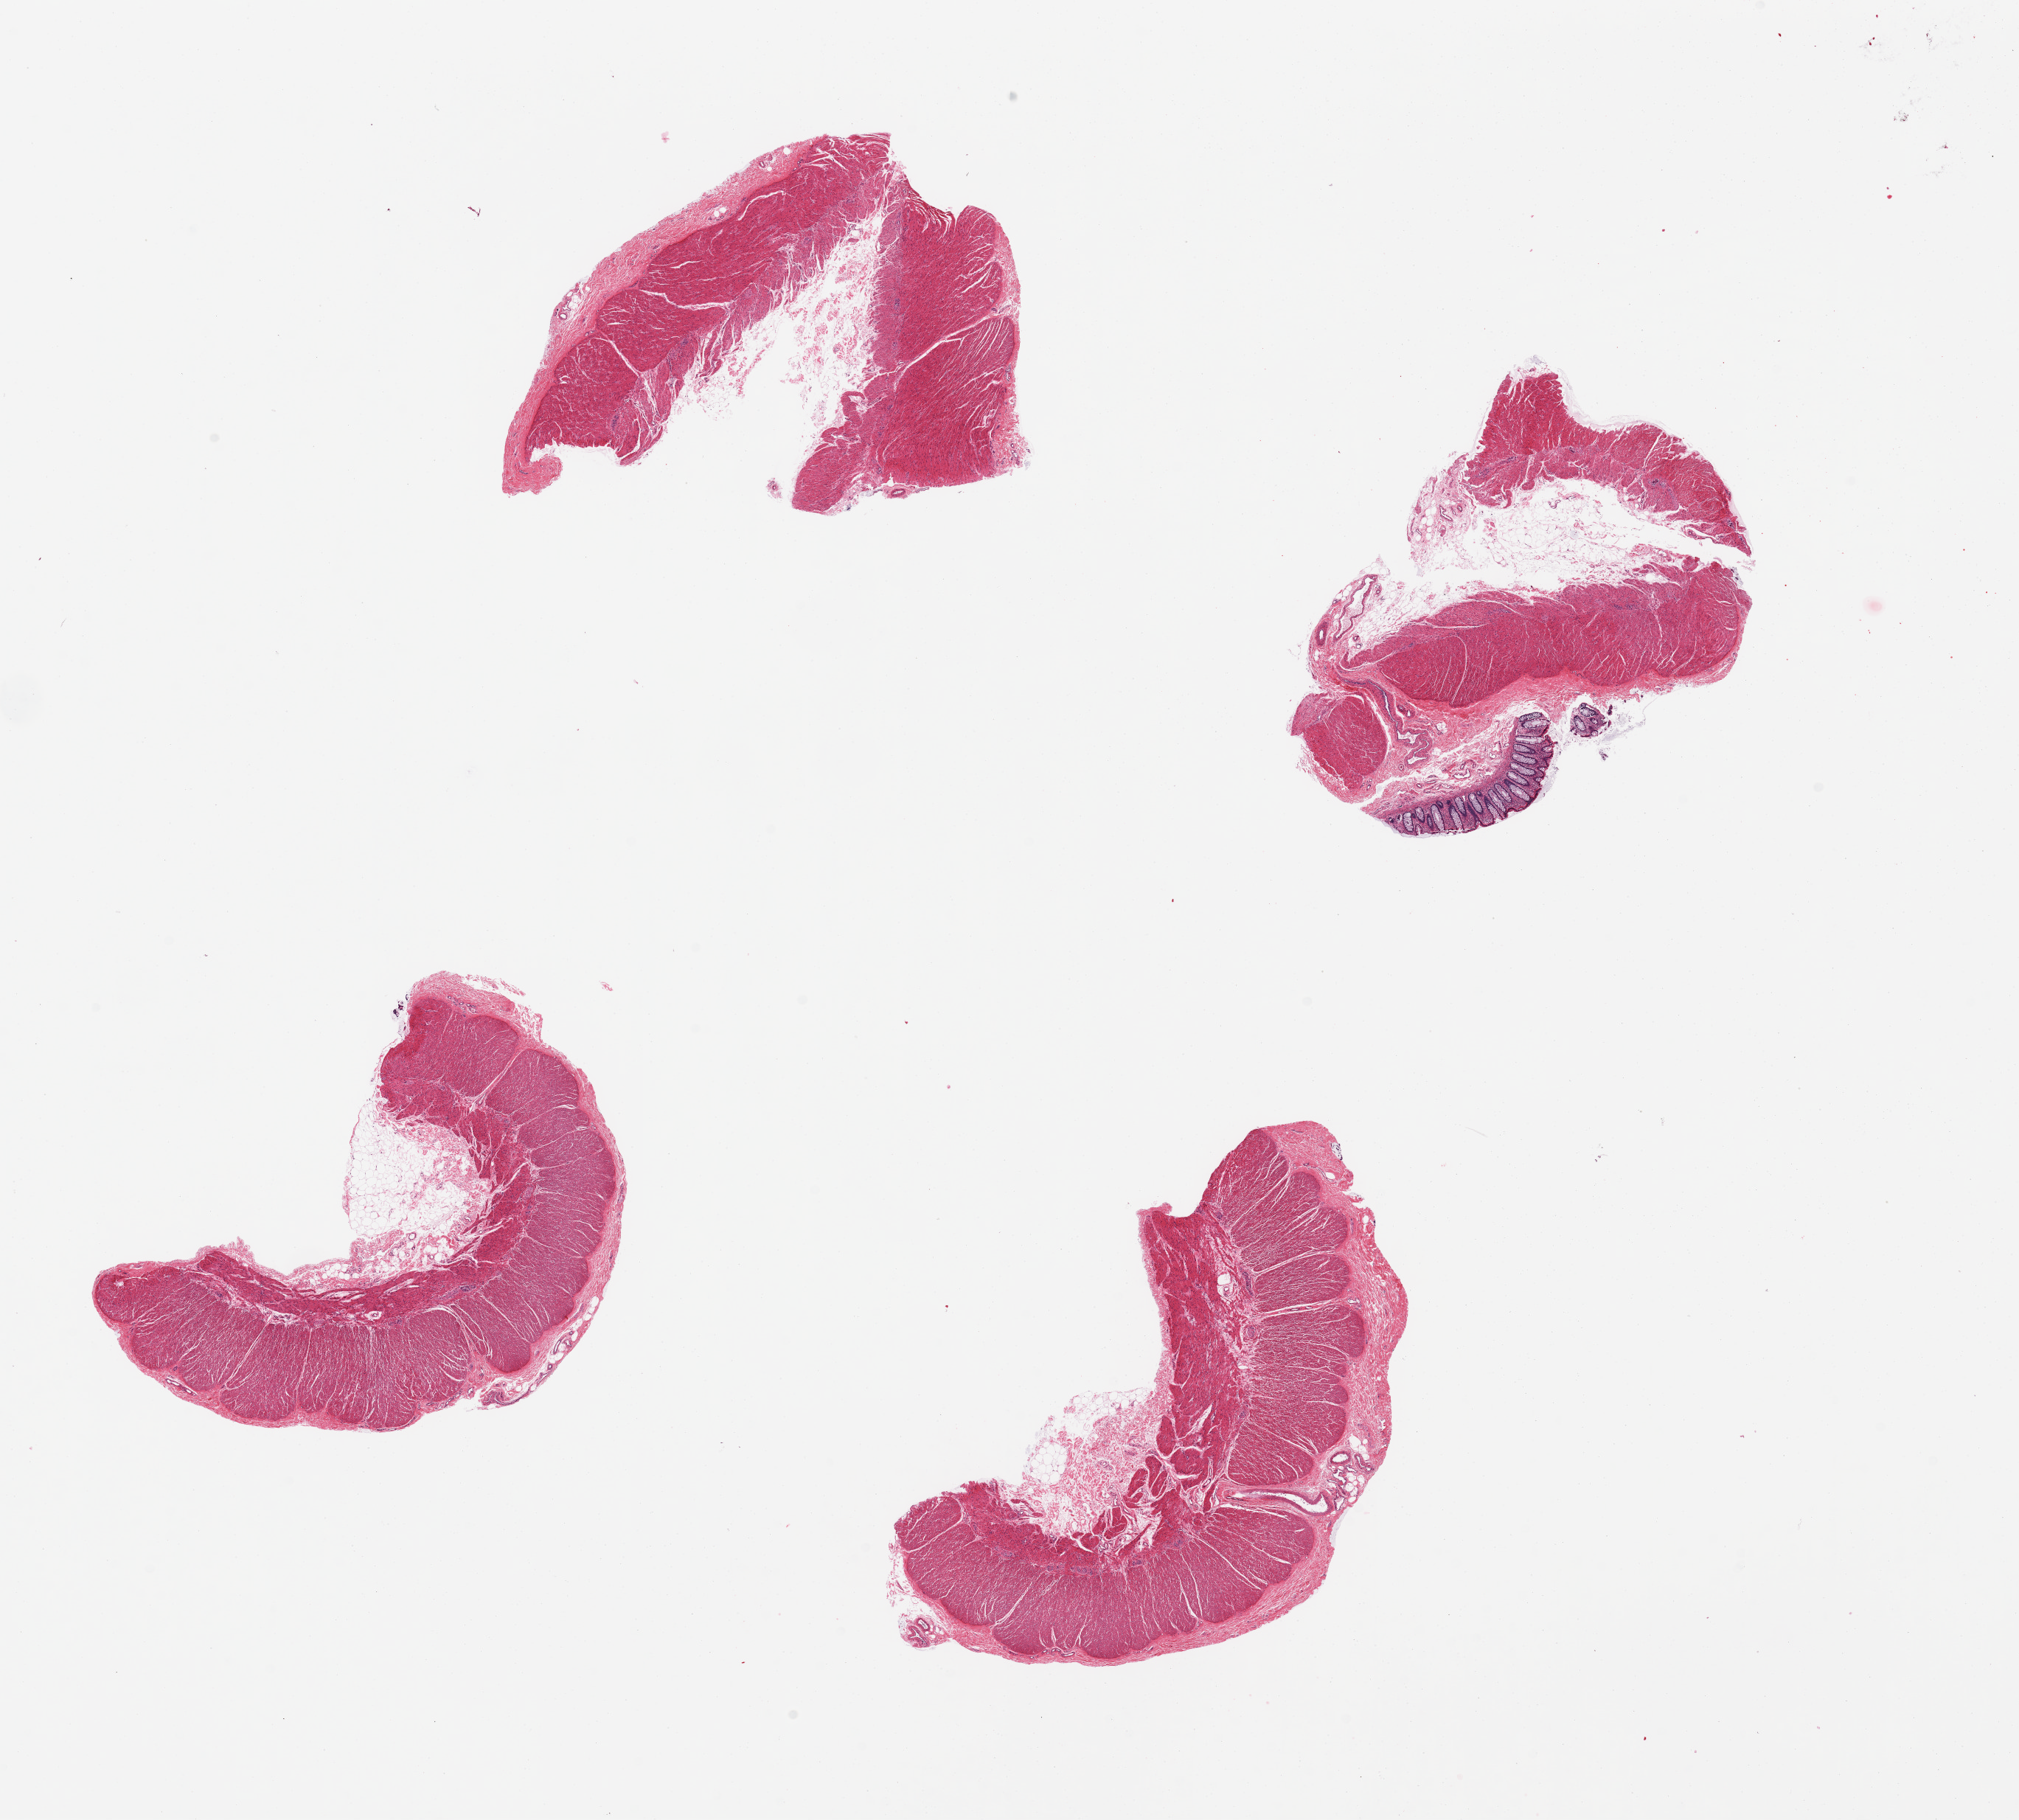
Whole-slide image, H&E stain — a low-resolution overview of the entire scanned area, about 21.7 x 19.5 mm (acquisition: 20x scan); PAXgene-fixed, paraffin-embedded tissue; sampled site (target tissue): sigmoid colon; tissue donor sample.
• reviewer comment on this tissue sample: 4 pieces, mainly muscularis; trace 'contaminant' mucosa